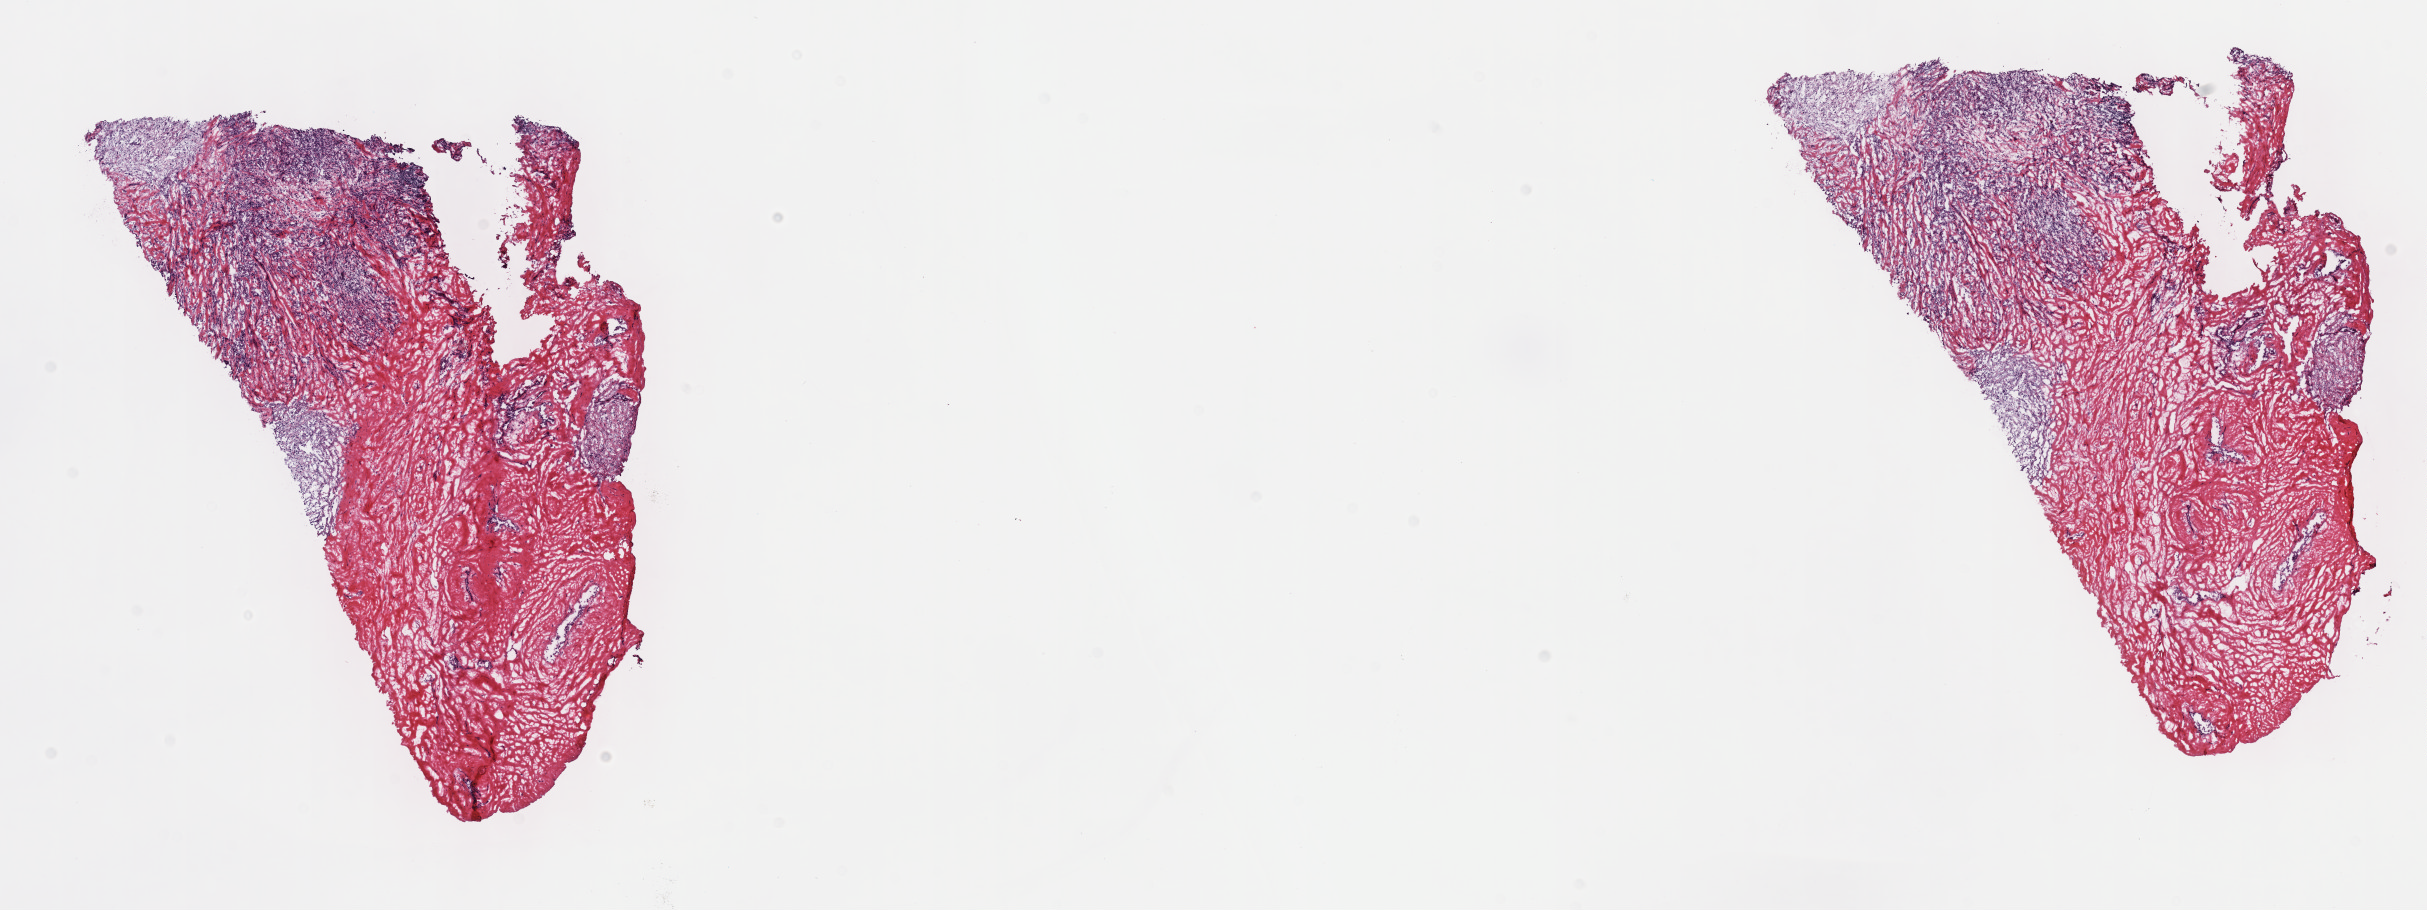
Whole-slide histology image, H&E, whole scanned area (about 19.6 x 7.4 mm) shown as a low-resolution overview. Frozen section from the top of the tissue portion. Breast, primary tumour sample. Female patient; age at initial diagnosis 63 years. Composition of this section per pathologist review: tumour cells 60%, tumour nuclei 60%, normal cells 0%, stromal cells 35%, necrosis 5%. Inflammatory infiltration, as recorded: lymphocyte infiltration 40%, monocyte infiltration 20%, neutrophil infiltration 20%.
- diagnosis: Lobular carcinoma, NOS
- AJCC pathologic stage: IV (7th edition)
- lymph nodes positive (case pathology): 0 of 1 examined
- laterality: left